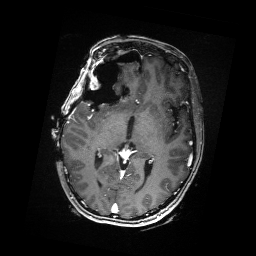
Brain MRI from a brain-tumour surgery series, one axial slice; position 95 of 176 along the scan axis; T1-weighted post-contrast; 1 mm slice thickness; 256 × 256 image matrix, field of view 256 × 256 mm. Case-level facts recorded for this patient, not image findings: histopathology: Metastatic Carcinoma from Breast primary.
Structures marked on this image (outlined manually by an expert reader):
- residual tumour: bounding box (x1, y1, x2, y2) in pixels: (98, 68, 110, 88)